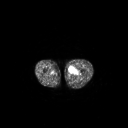
FDG PET of an extremity soft-tissue mass (from a PET/CT study), one axial slice; slice 226 of 267 in the series (ordered by position); 128 × 128 image matrix, field of view 700 × 700 mm. Patient: male, 63 years. Case-level facts recorded for this patient, not image findings: histological type: pleiomorphic liposarcoma; grade: high; site of the primary tumour: left thigh.
Structures marked on this image (expert contour drawn on MRI and transferred to this co-registered scan by the dataset authors):
- gross tumour volume including surrounding oedema: bounding box (x1, y1, x2, y2) in pixels: (69, 66, 79, 75)
- gross tumour volume (mass): (69, 66, 75, 72)